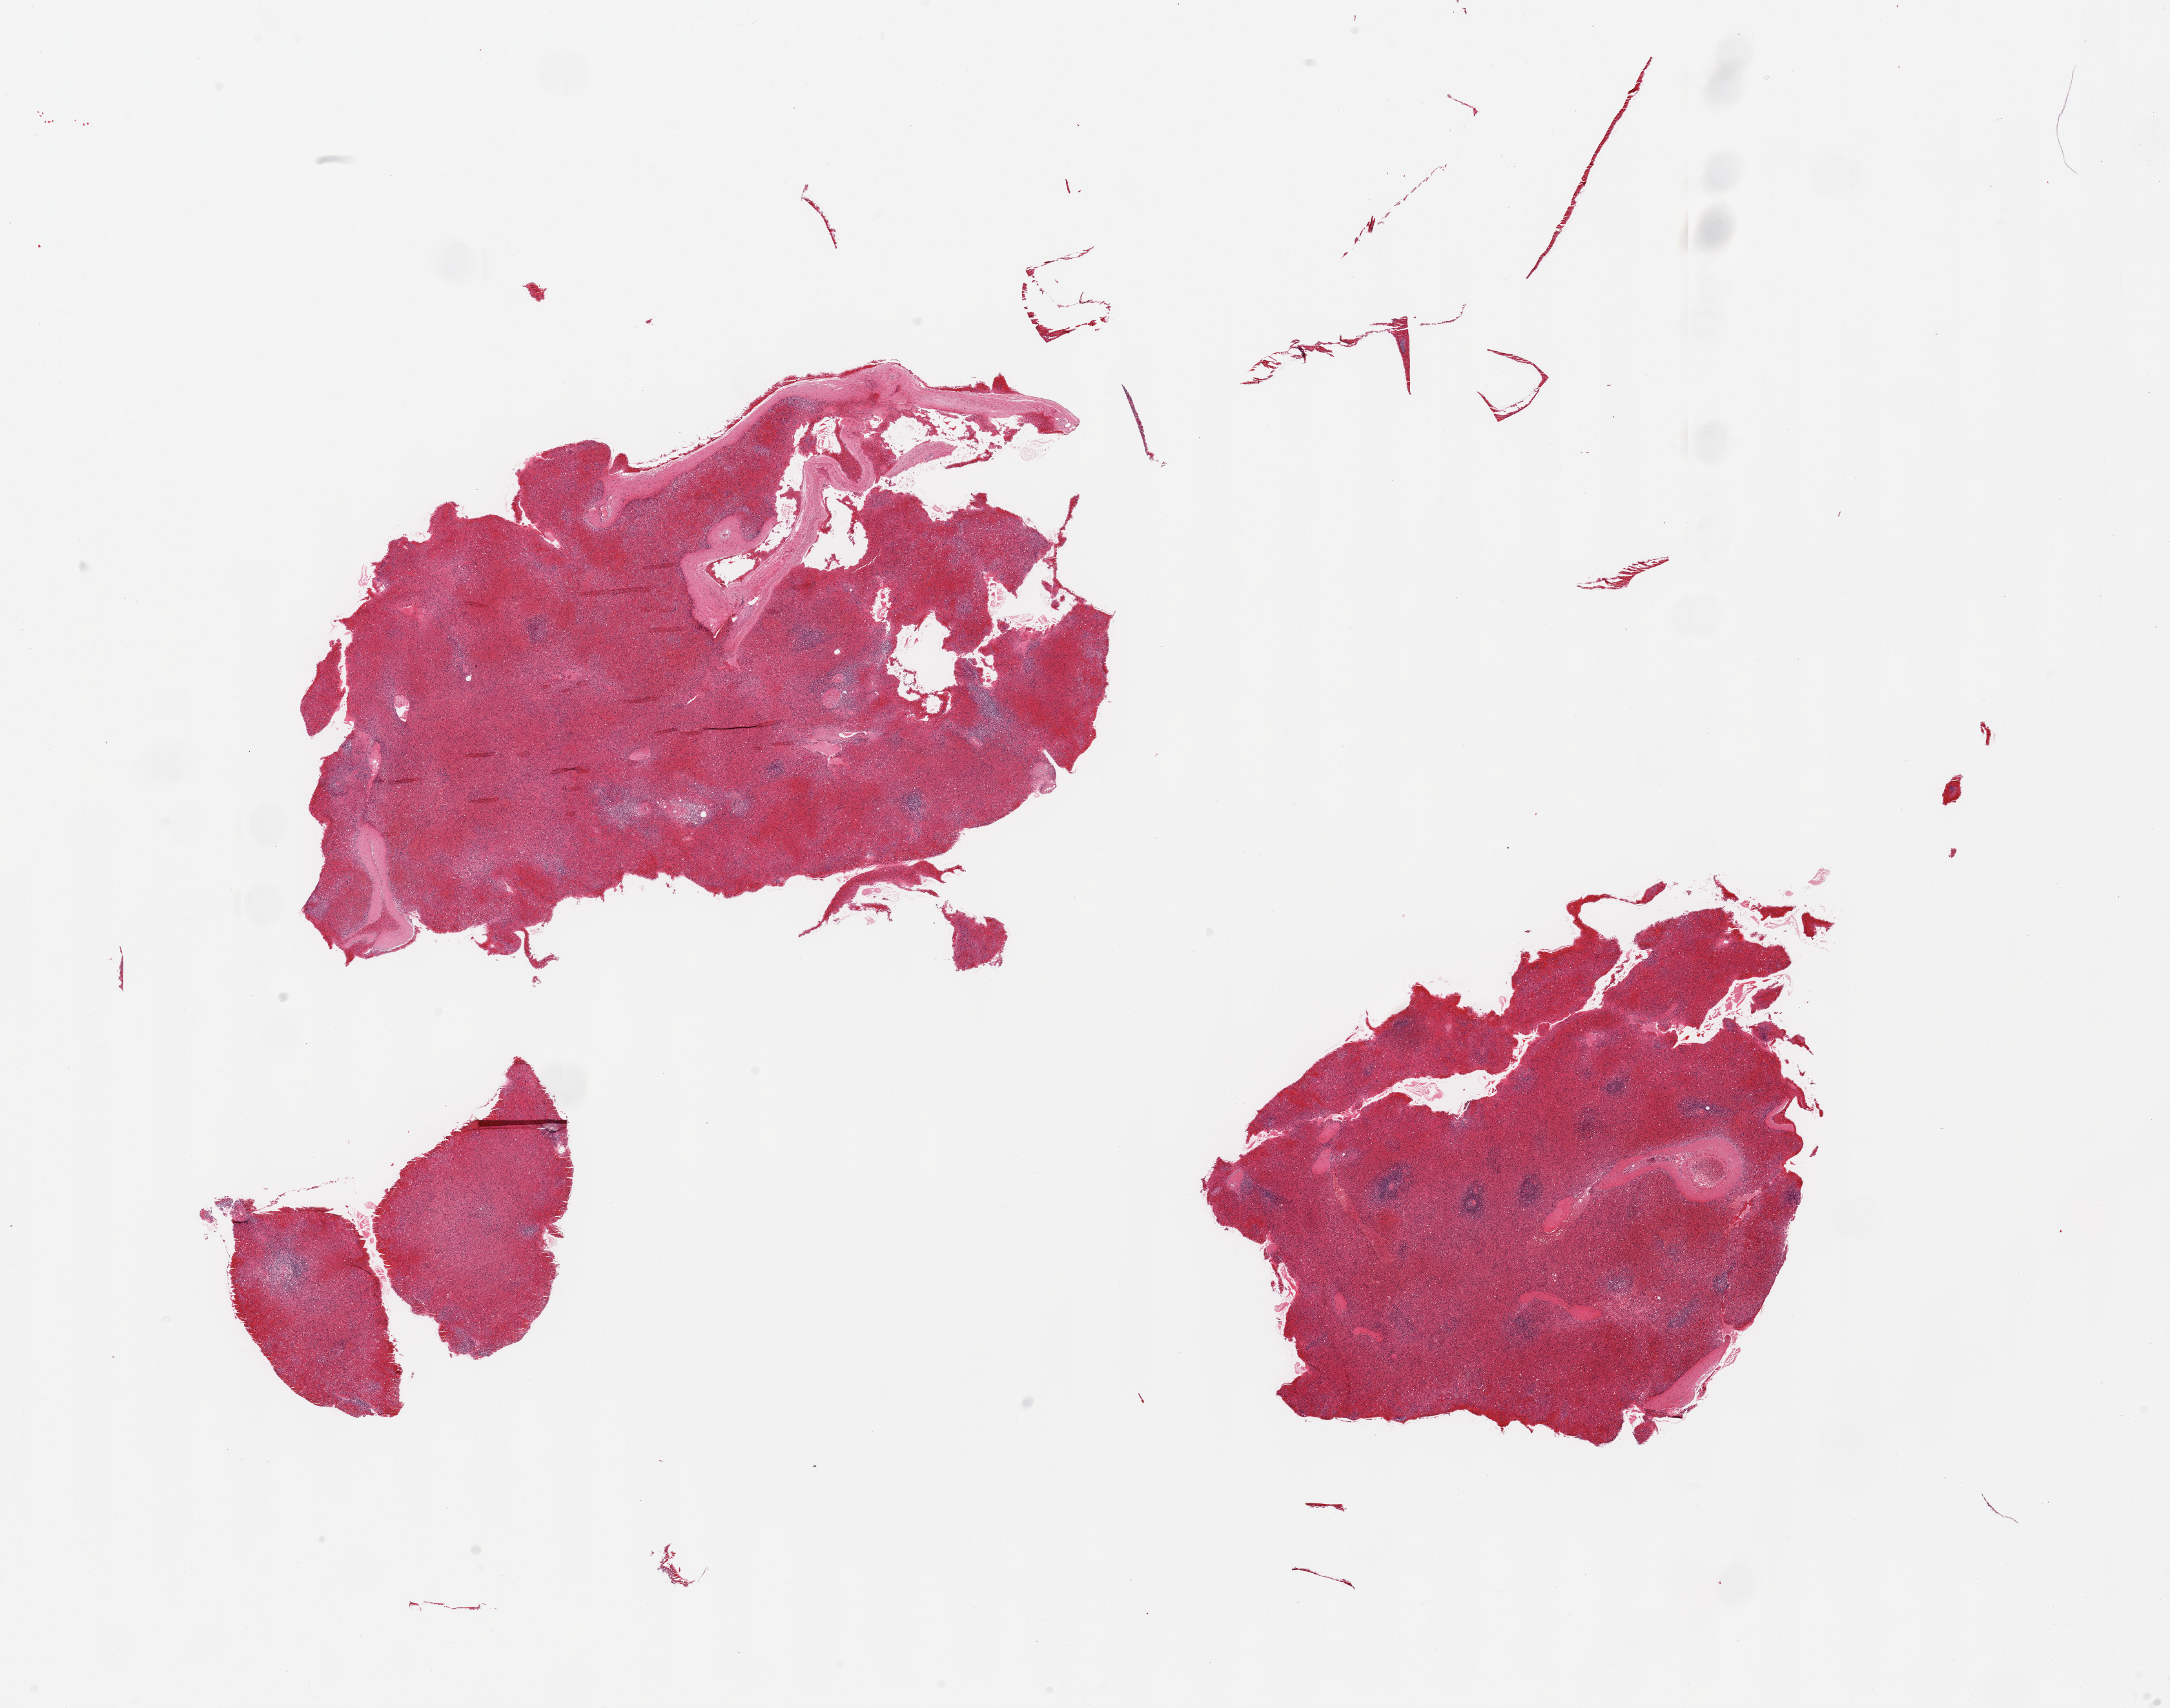
Digitized H&E-stained section — shown as a low-resolution overview of the whole scanned area (about 26.6 x 20.9 mm); PAXgene-fixed, paraffin-embedded tissue; target tissue: spleen; tissue donor sample. Donor sex: male.
Review note (as recorded): 2 pieces & fragments; severe congestion.